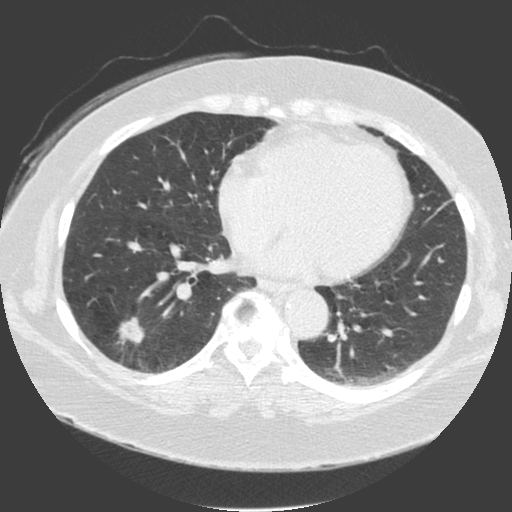
Low-dose screening chest CT, one axial slice. Position 73 of 175 along the scan axis. 120 kVp. Lung window (W 1500 / L -600 HU). 2 mm slice thickness. 512 × 512 image matrix, field of view 370 × 370 mm.
Outlined on this slice (outlined manually by an expert reader):
- lesion 1 (tumor, lower lobe of right lung): bounding box [x1, y1, x2, y2] px = [119, 318, 144, 344]